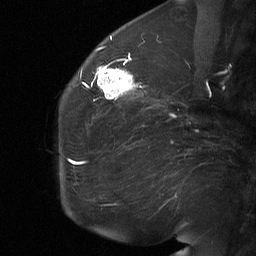
Breast MRI (dynamic contrast-enhanced), one sagittal slice; position 23 of 64 along the scan axis; dynamic contrast-enhanced study with each time point stored as its own series, time point 2 of 3 at this slice position (early post-contrast, ordered by acquisition time); 1.5 T; TE 4.8 ms, TR 27 ms; 2 mm slice thickness; 256 × 256 image matrix, field of view 200 × 200 mm. Female patient, age 60 years. Case-level facts recorded for this patient, not image findings: setting: breast cancer imaged before/during neoadjuvant chemotherapy; receptor status: HR-positive, HER2-negative.
Annotated regions visible in this slice (semi-automatic segmentation, software-assisted and operator-edited):
- analysis volume of interest (the breast-tissue region the enhancement analysis was run in; not a lesion): box from (x=91, y=56) to (x=139, y=104) px
- tumour enhancement mask (voxels above the 90 % enhancement threshold inside the analysis volume of interest): (x=91, y=65)–(x=137, y=100)